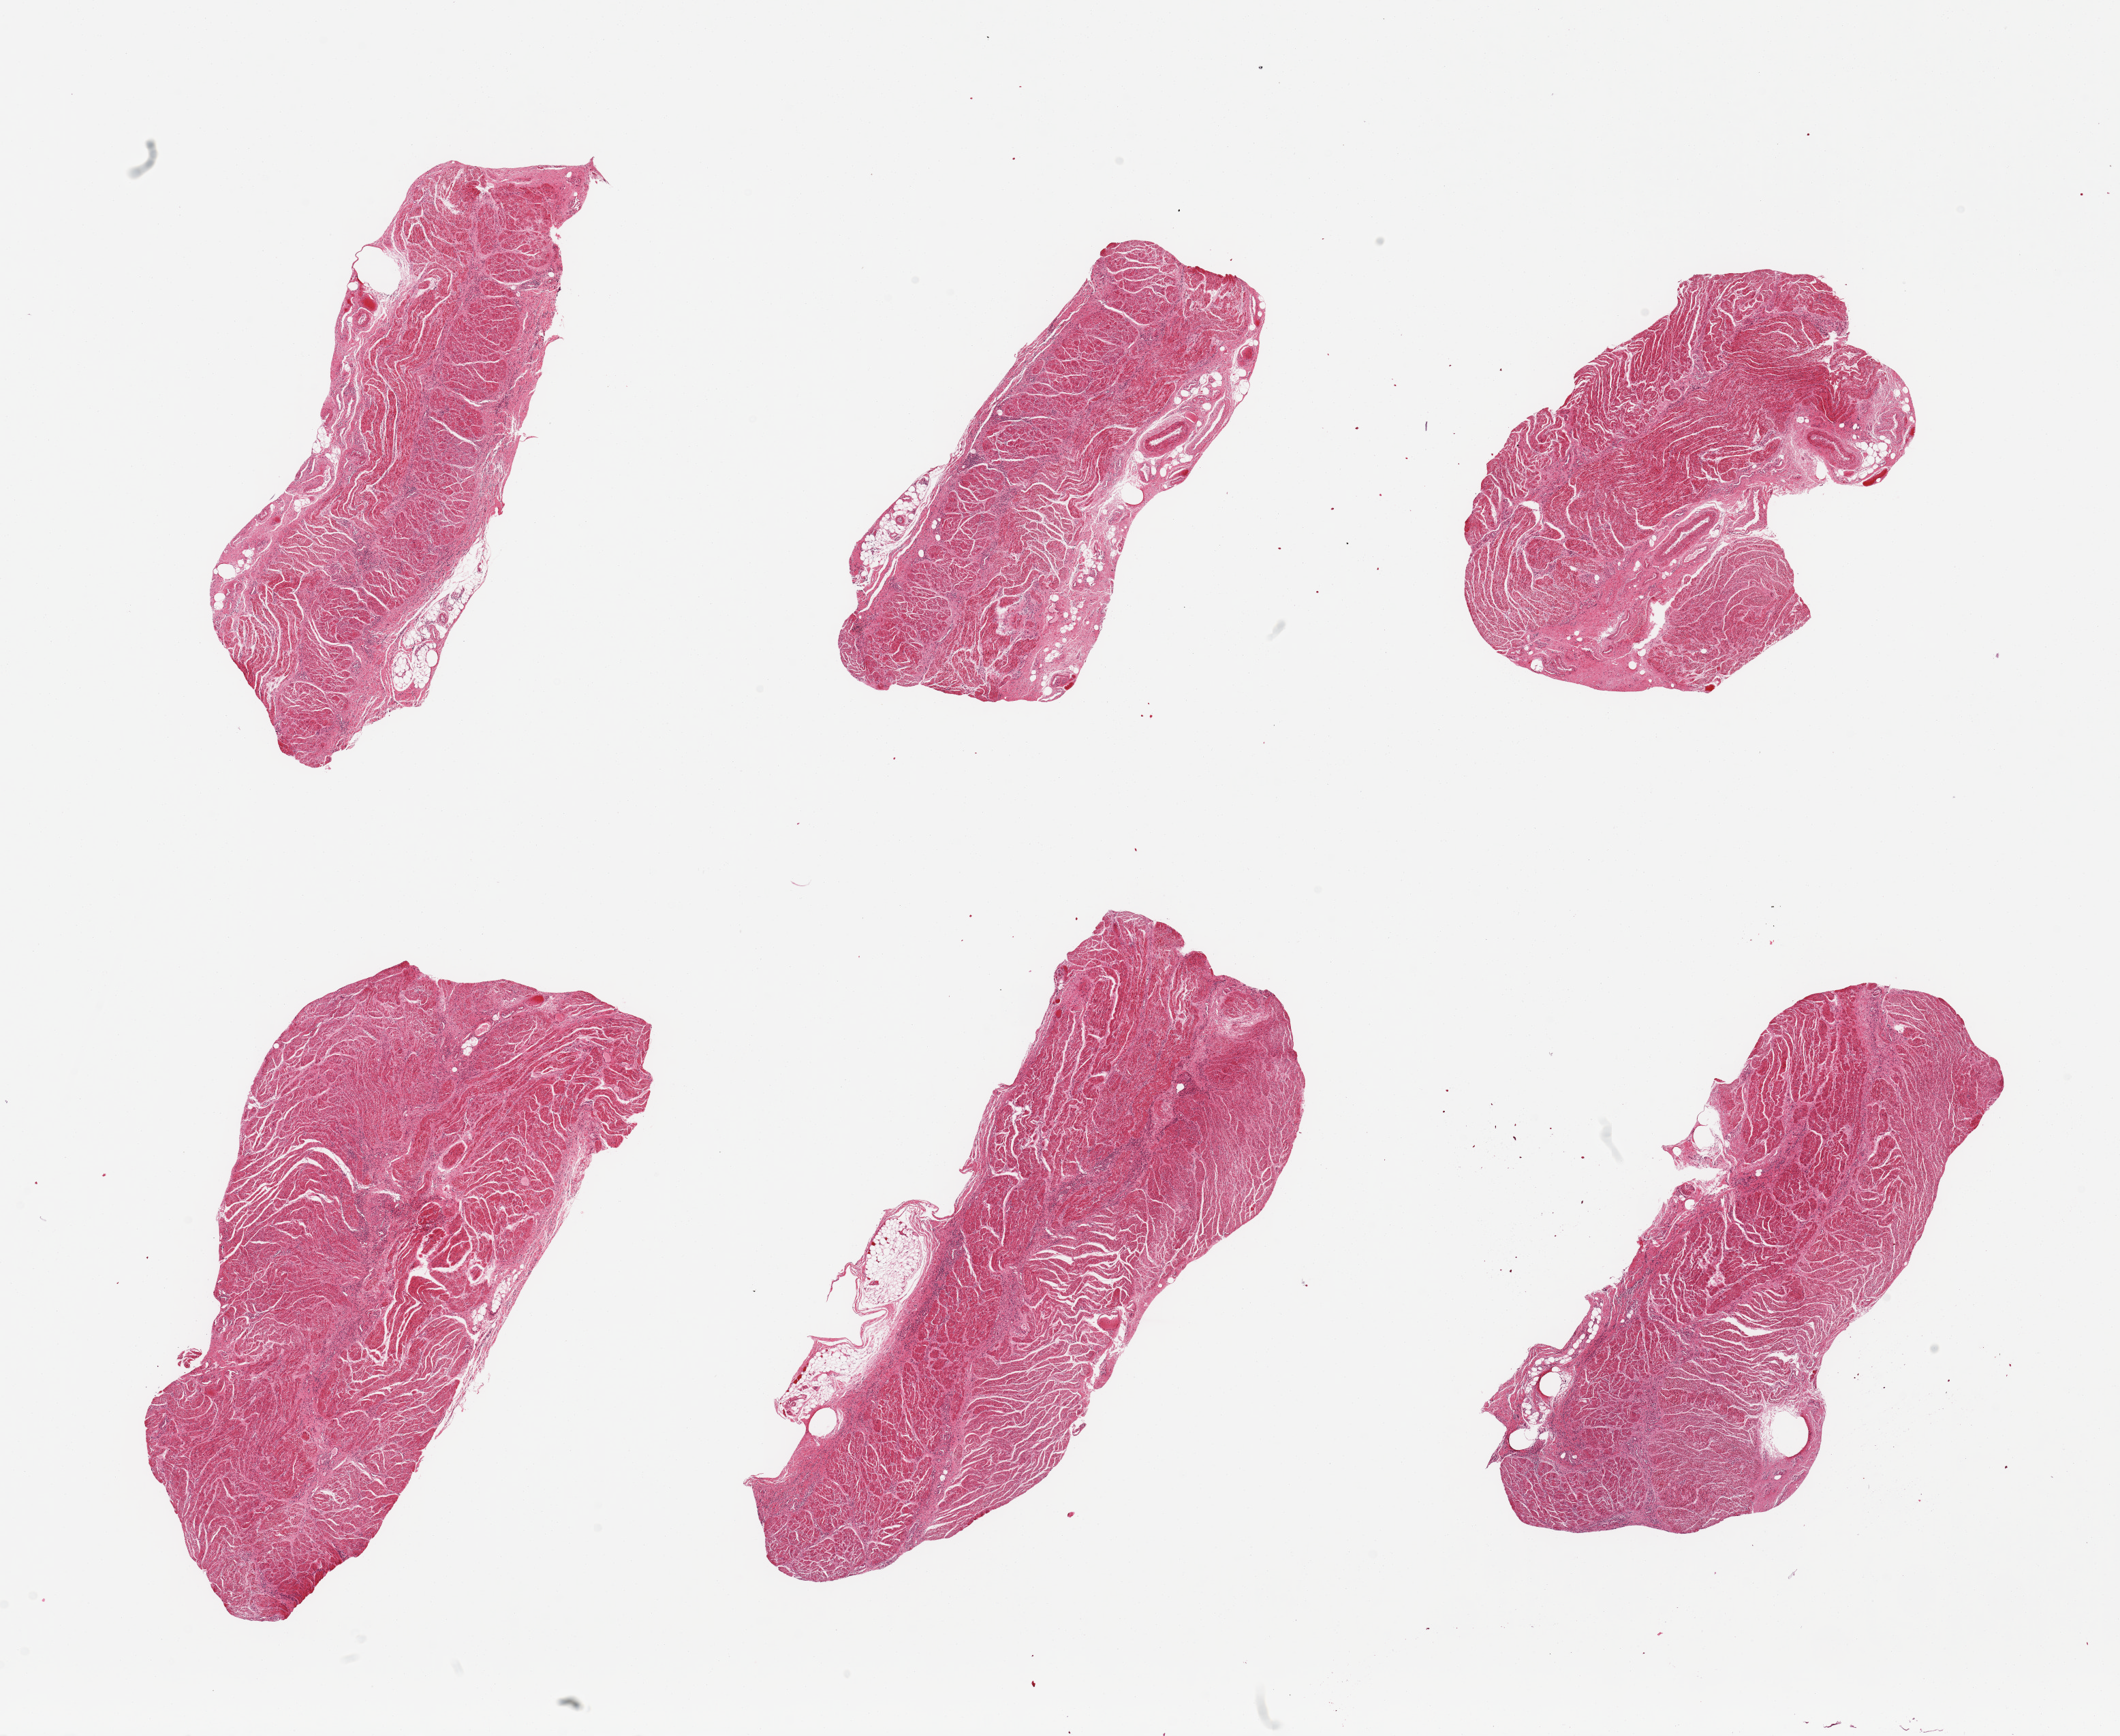
Digitized H&E-stained section, brightfield — whole scanned area (about 24.6 x 20.2 mm) shown as a low-resolution overview. PAXgene-fixed paraffin-embedded (PFPE) section. Sampled site (target tissue): gastroesophageal junction. Donor tissue sample. Male donor.
• pathologist's review note for this sample: 6 pieces, confirmed target muscularis